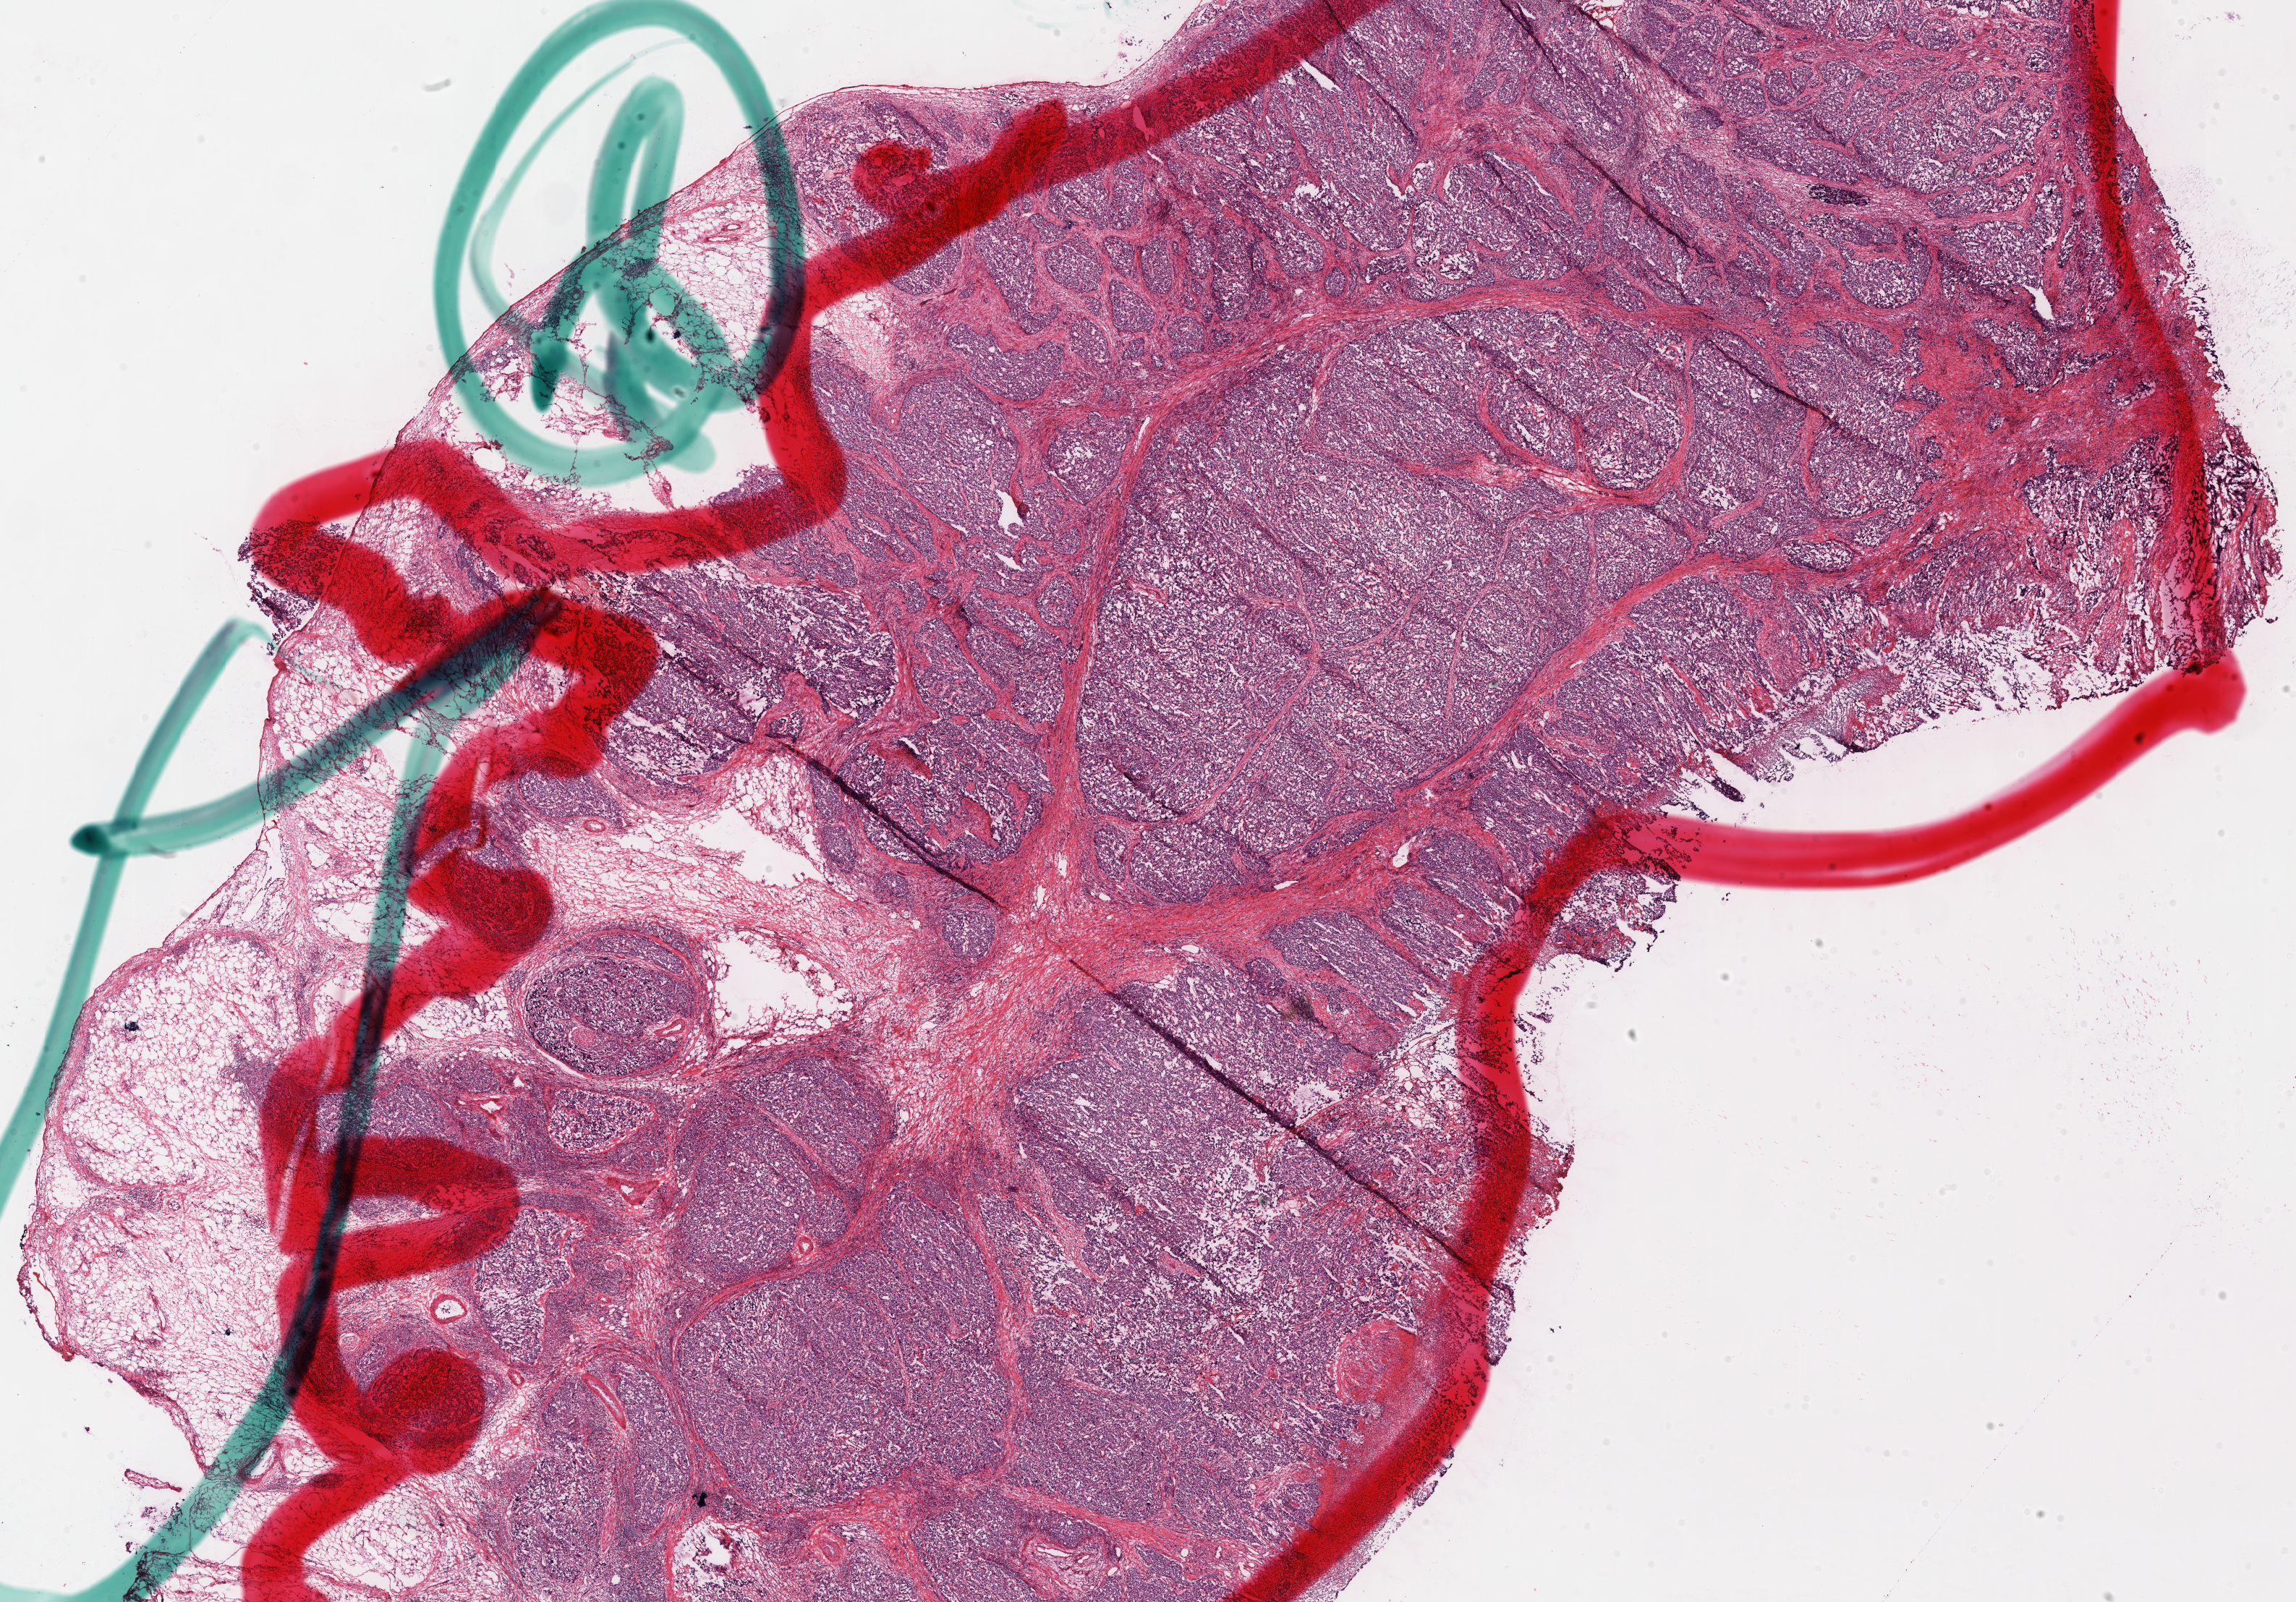
Whole-slide histology image, Hematoxylin and eosin (H&E) stained — low-resolution overview of the scanned area, about 25.0 x 17.4 mm (slide scanned at 40x). Frozen section from the top of the tissue portion. Stomach, primary tumour sample. Male patient; age at initial diagnosis 59 years. Histologic grade: G3 (poorly differentiated). Pathologist review of this section (percent, as recorded): tumour cells 100%, tumour nuclei 70%, normal cells 0%, stromal cells 0%, necrosis 0%. Infiltration values recorded for this section: lymphocyte infiltration 15%, monocyte infiltration 0%, neutrophil infiltration 10%.
* histologic diagnosis: Adenocarcinoma, NOS (body of stomach)
* AJCC pathologic stage: IIIB (7th edition)